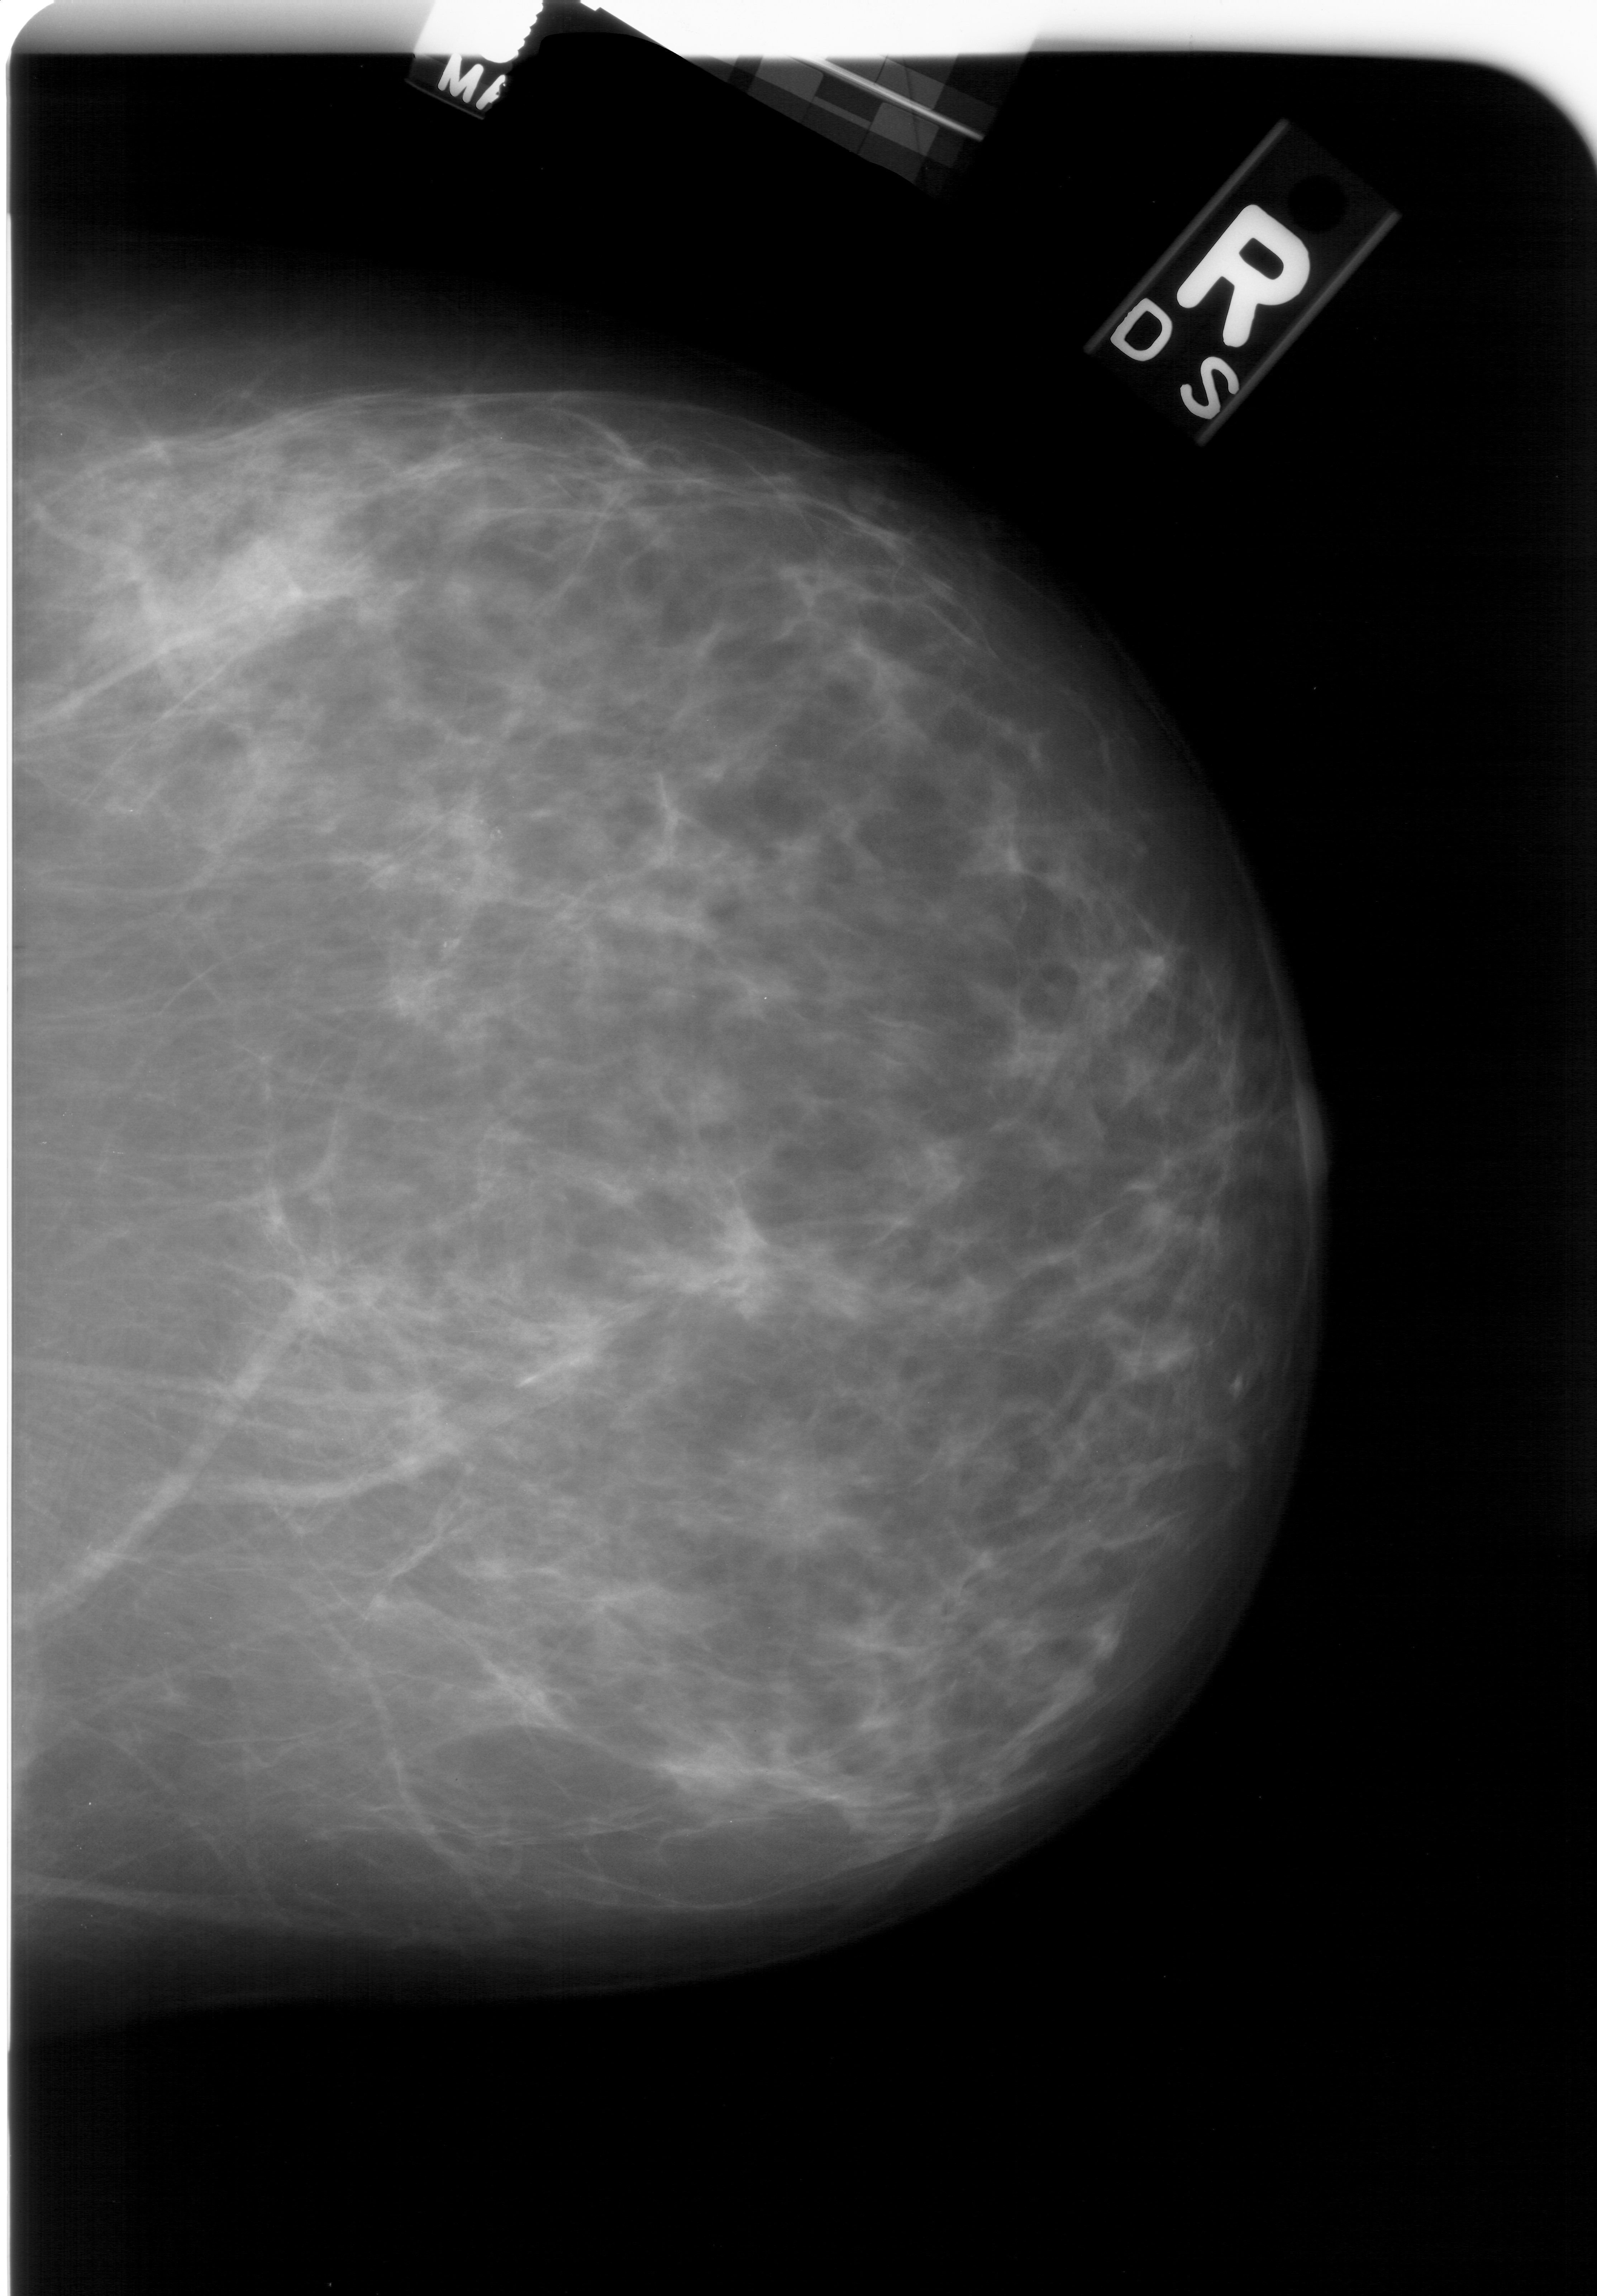
Digitized screen-film mammogram; right breast; craniocaudal (CC) view; BI-RADS breast density category 1 (scale 1–4); 1597 × 2296 image matrix.
Expert-marked regions of interest on this image (one box per marked abnormality):
- calcifications, morphology pleomorphic, distribution linear; BI-RADS assessment category 4; subtlety rating 3 on a 1 (subtle) to 5 (obvious) scale; pathology result (as recorded, not read from the image): malignant: bounding box (x1, y1, x2, y2) in pixels: (427, 792, 511, 973)